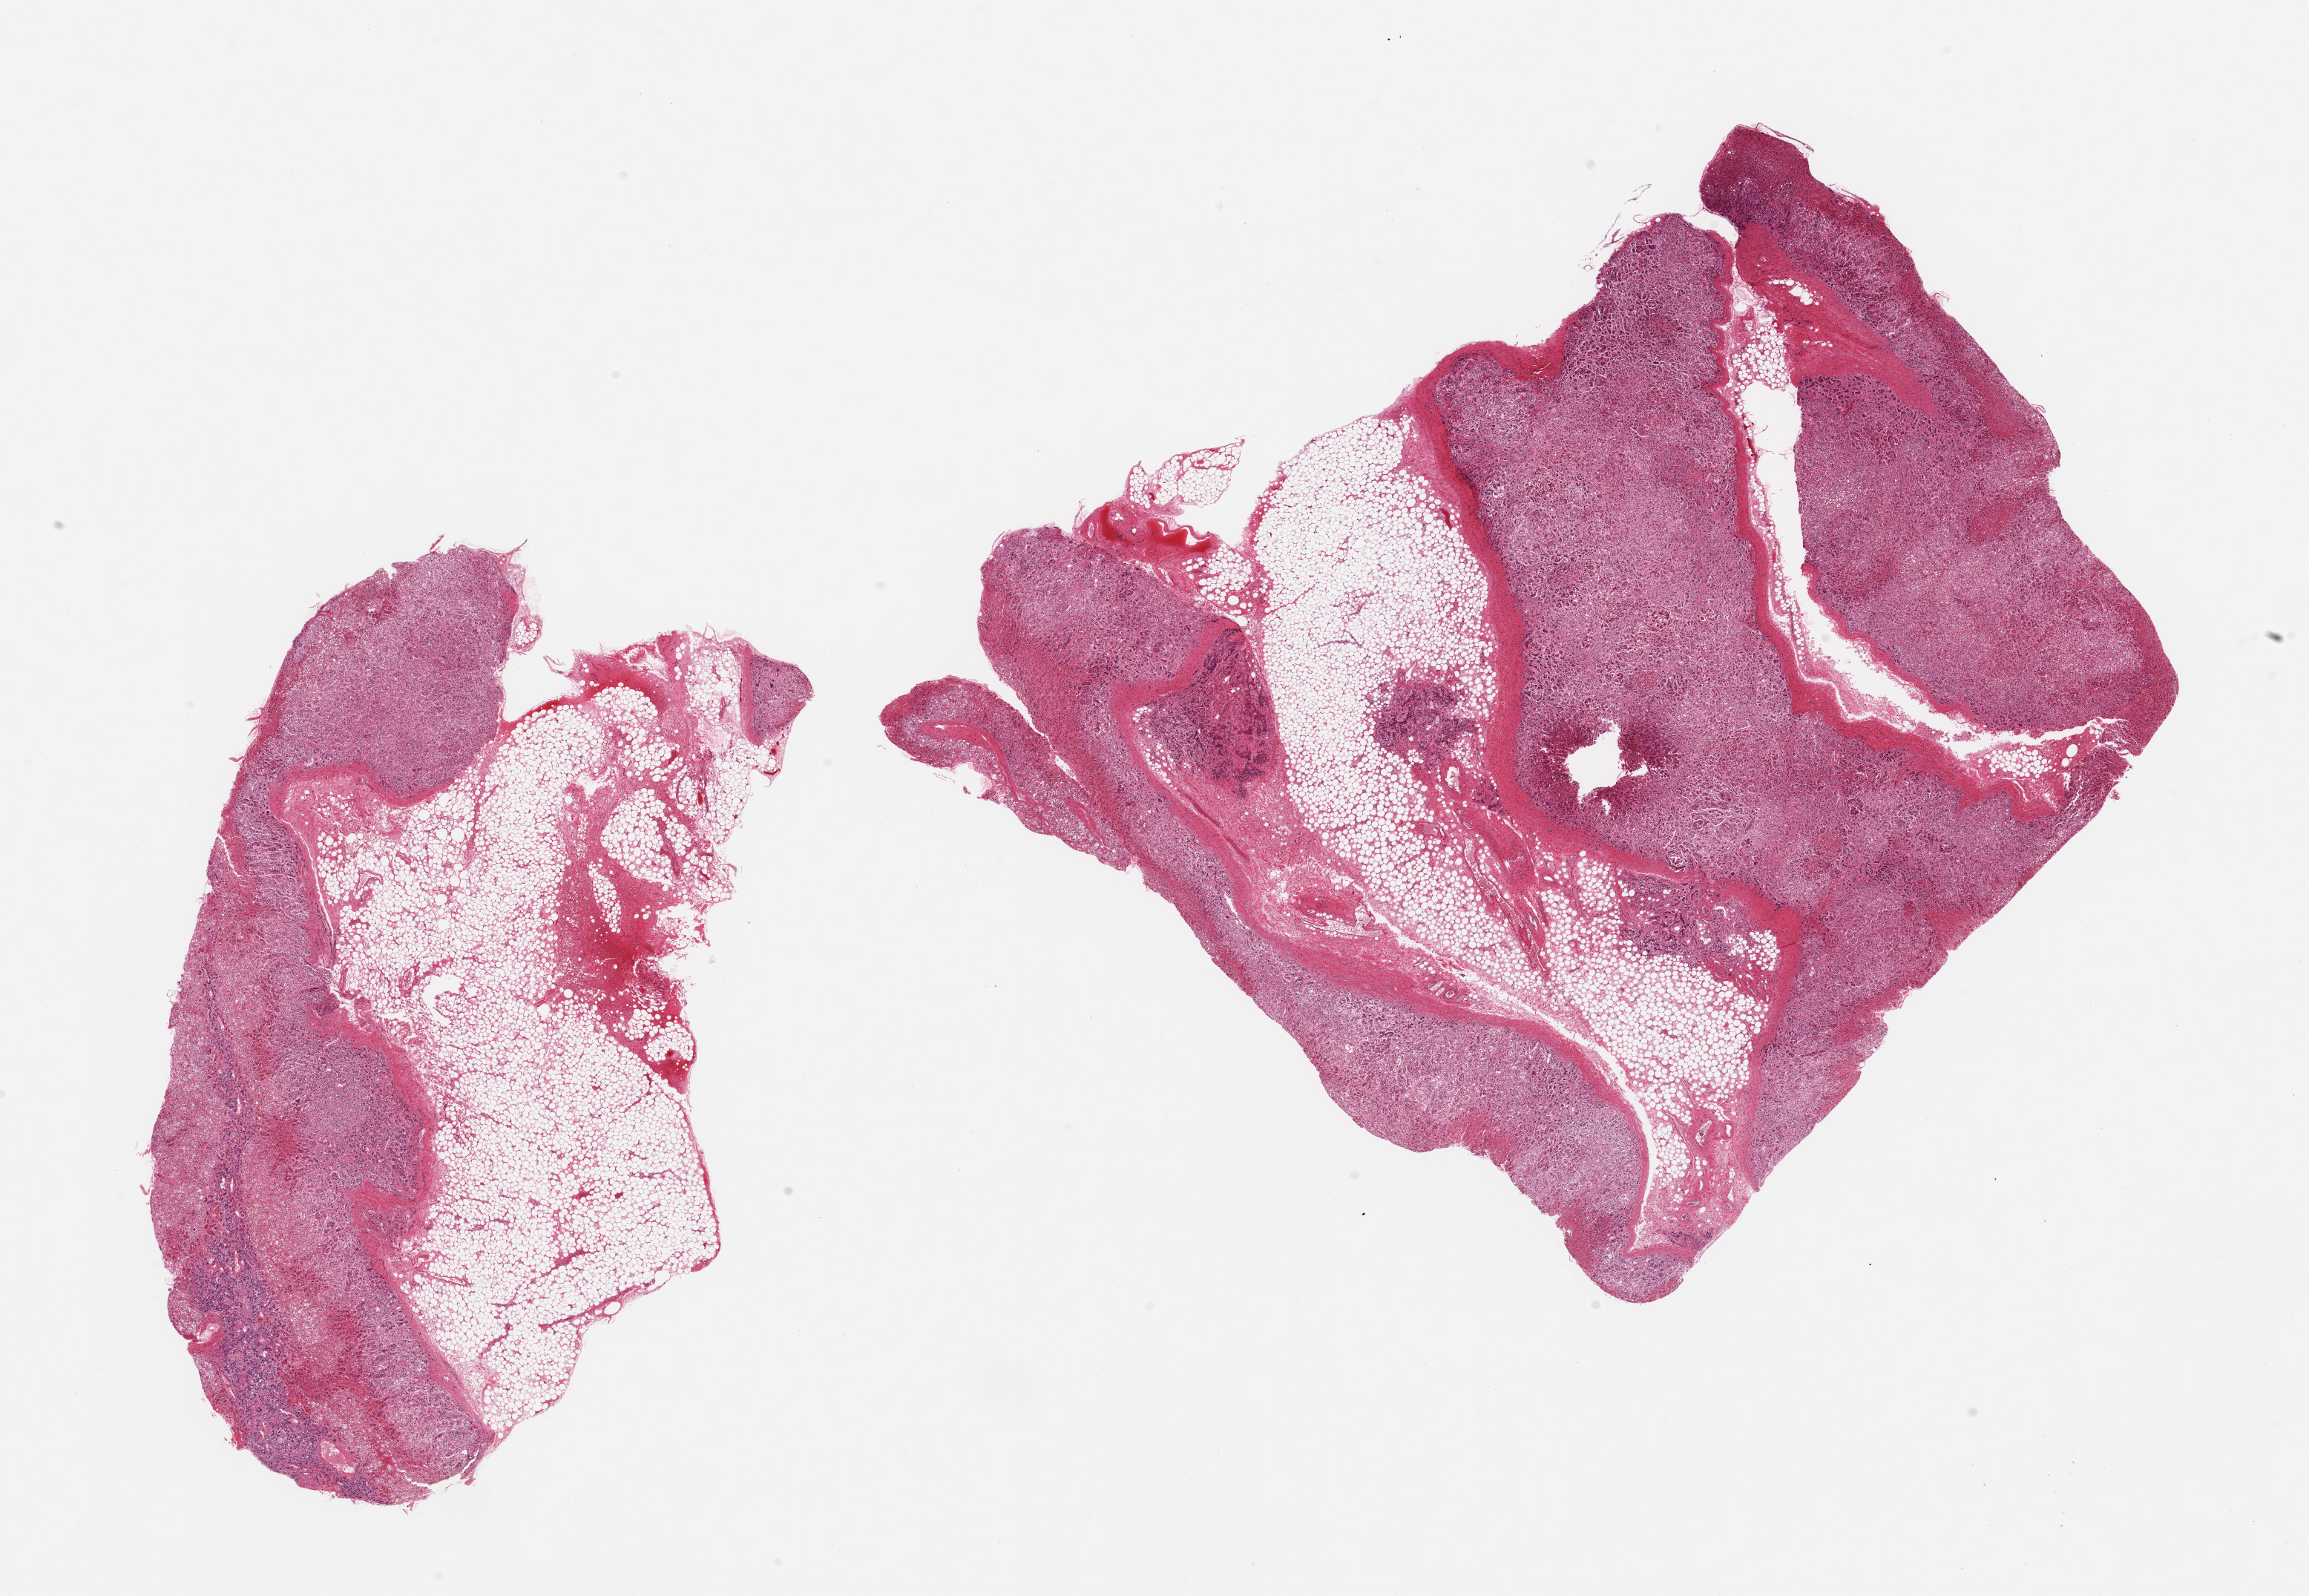
Haematoxylin and eosin whole-slide image, whole scanned area (about 24.6 x 17.0 mm, from a 20x scan) shown as a low-resolution overview; PAXgene-fixed paraffin-embedded (PFPE) section; sampled site (target tissue): adrenal gland; tissue donor sample. Donor: male.
• review note (as recorded): 2 pieces; moderately to severely autolyzed adrenal cortex and medulla; 50% and 40% fat content